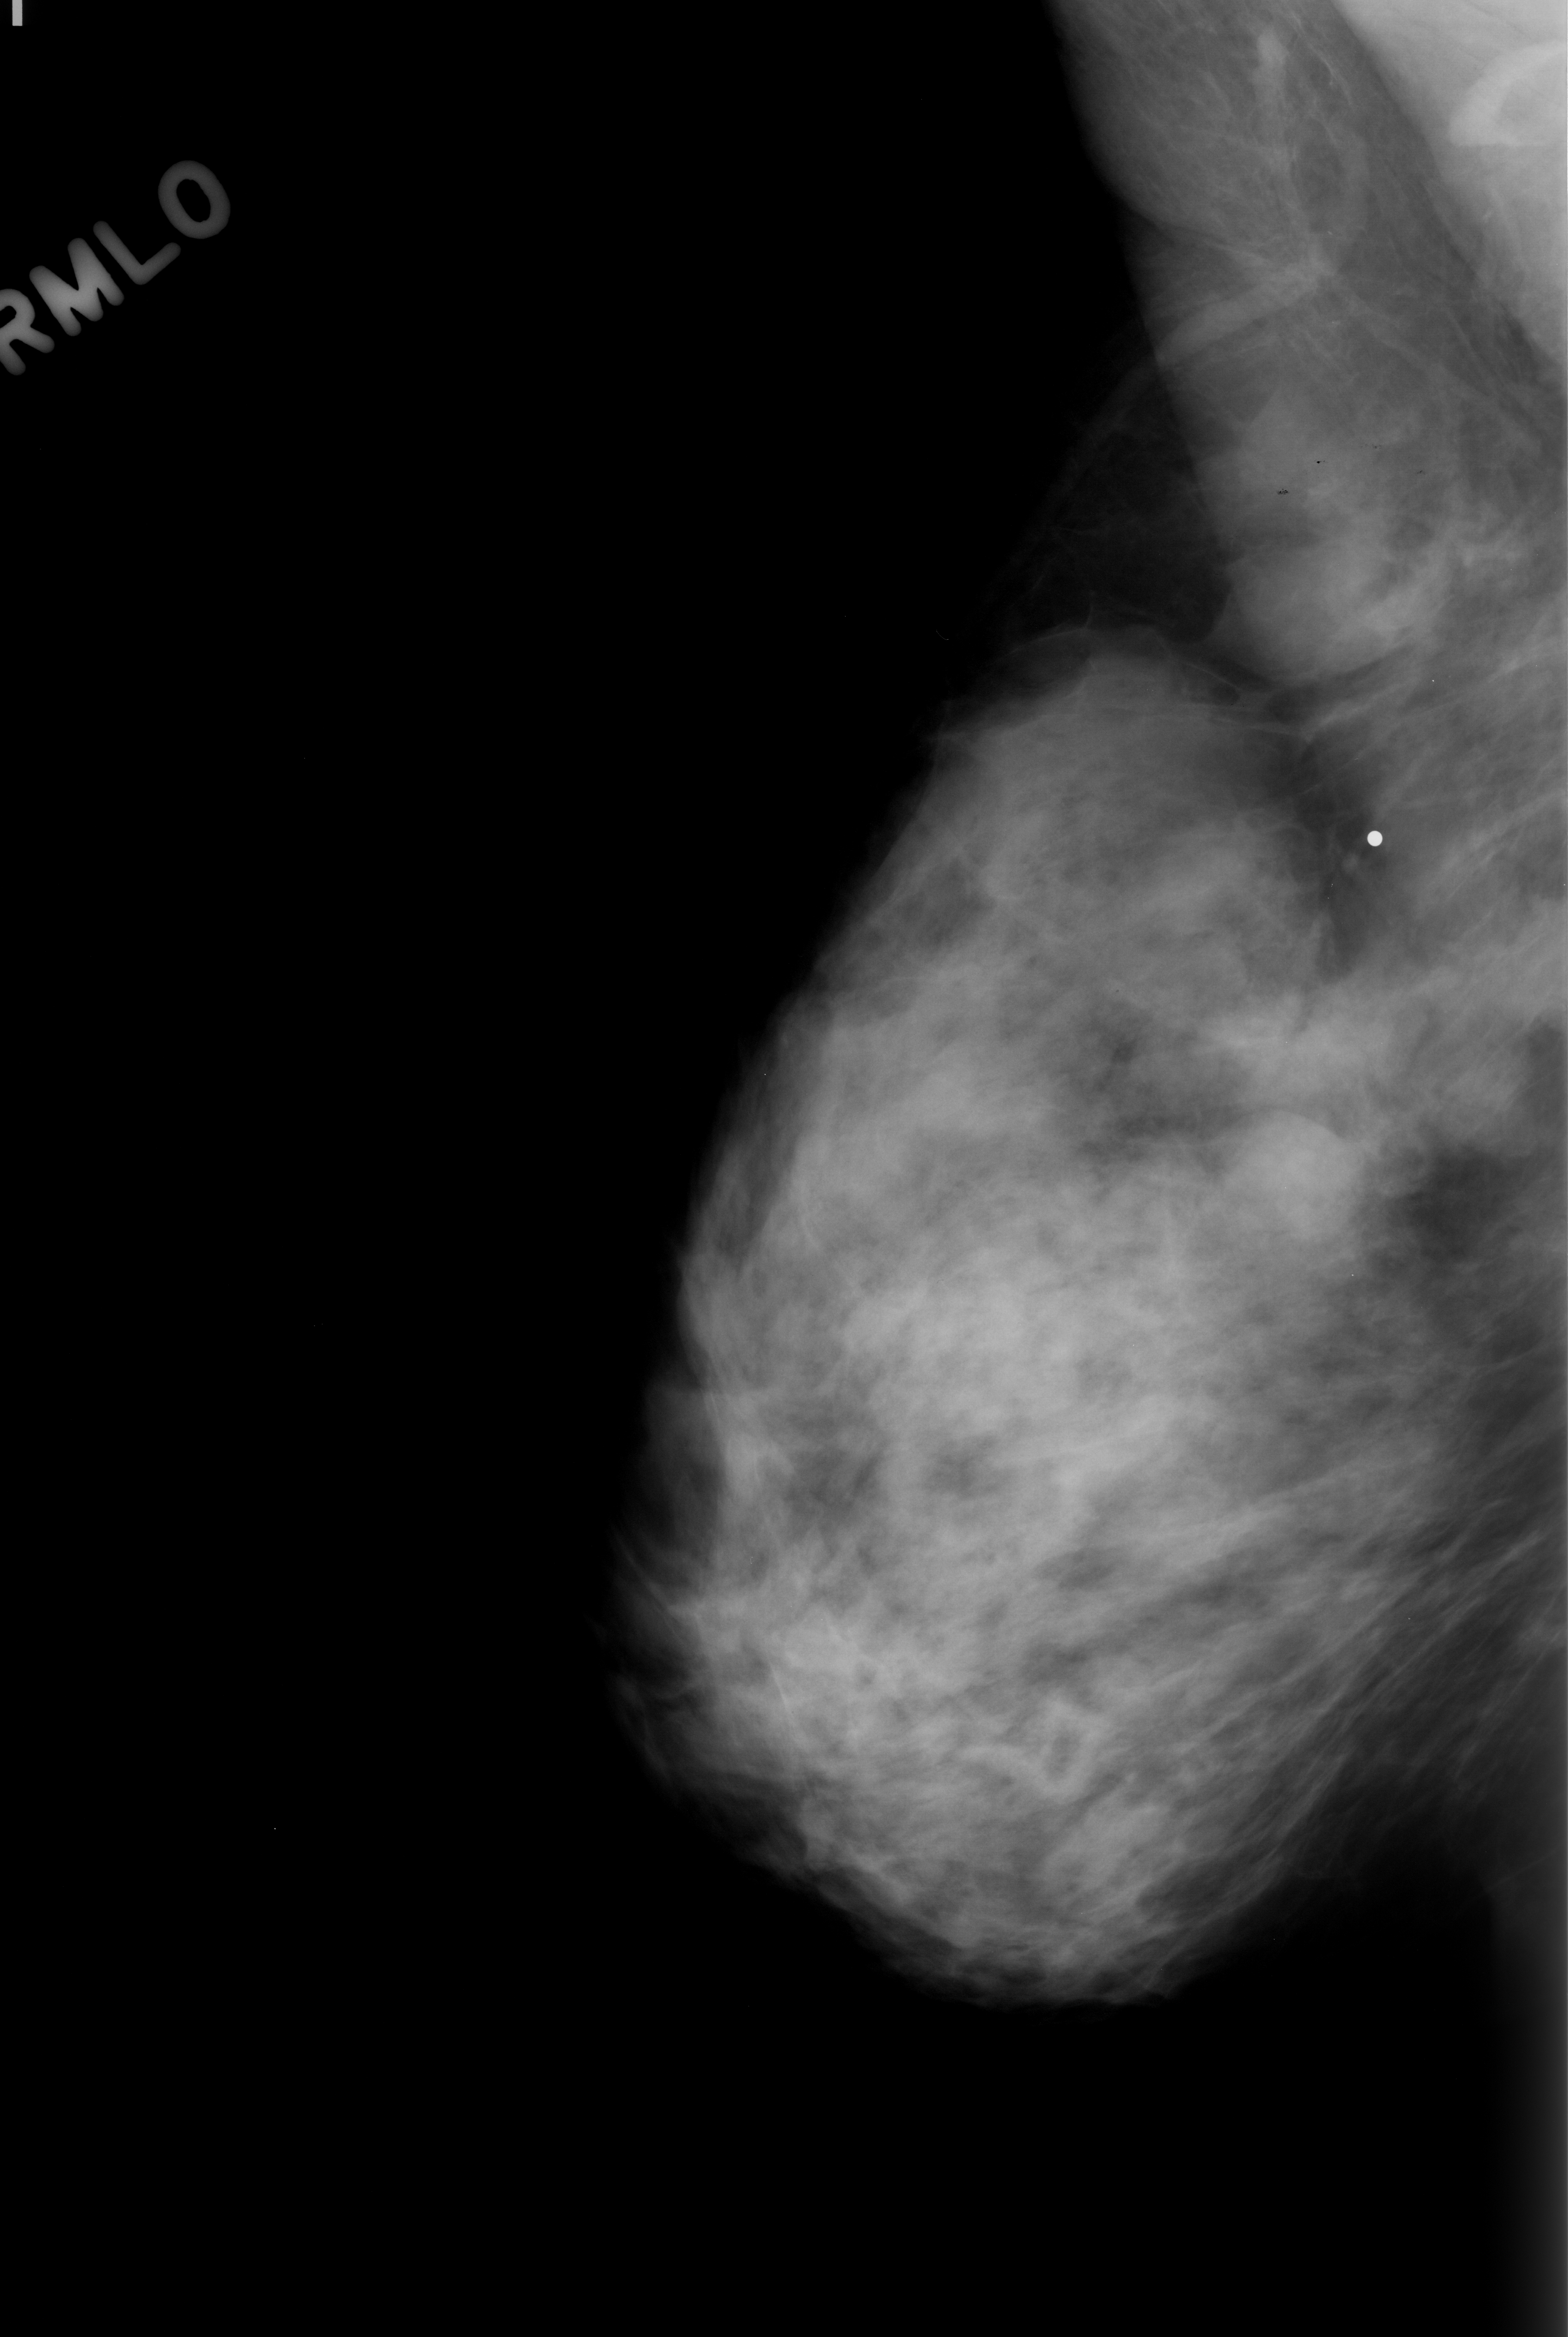
Mammogram (digitized film), right breast, MLO view, BI-RADS breast density category 3 (scale 1–4).
Finding: mass, shape oval, margins obscured; BI-RADS assessment category 3; subtlety rating 5 on a 1 (subtle) to 5 (obvious) scale; pathology (as recorded): benign.